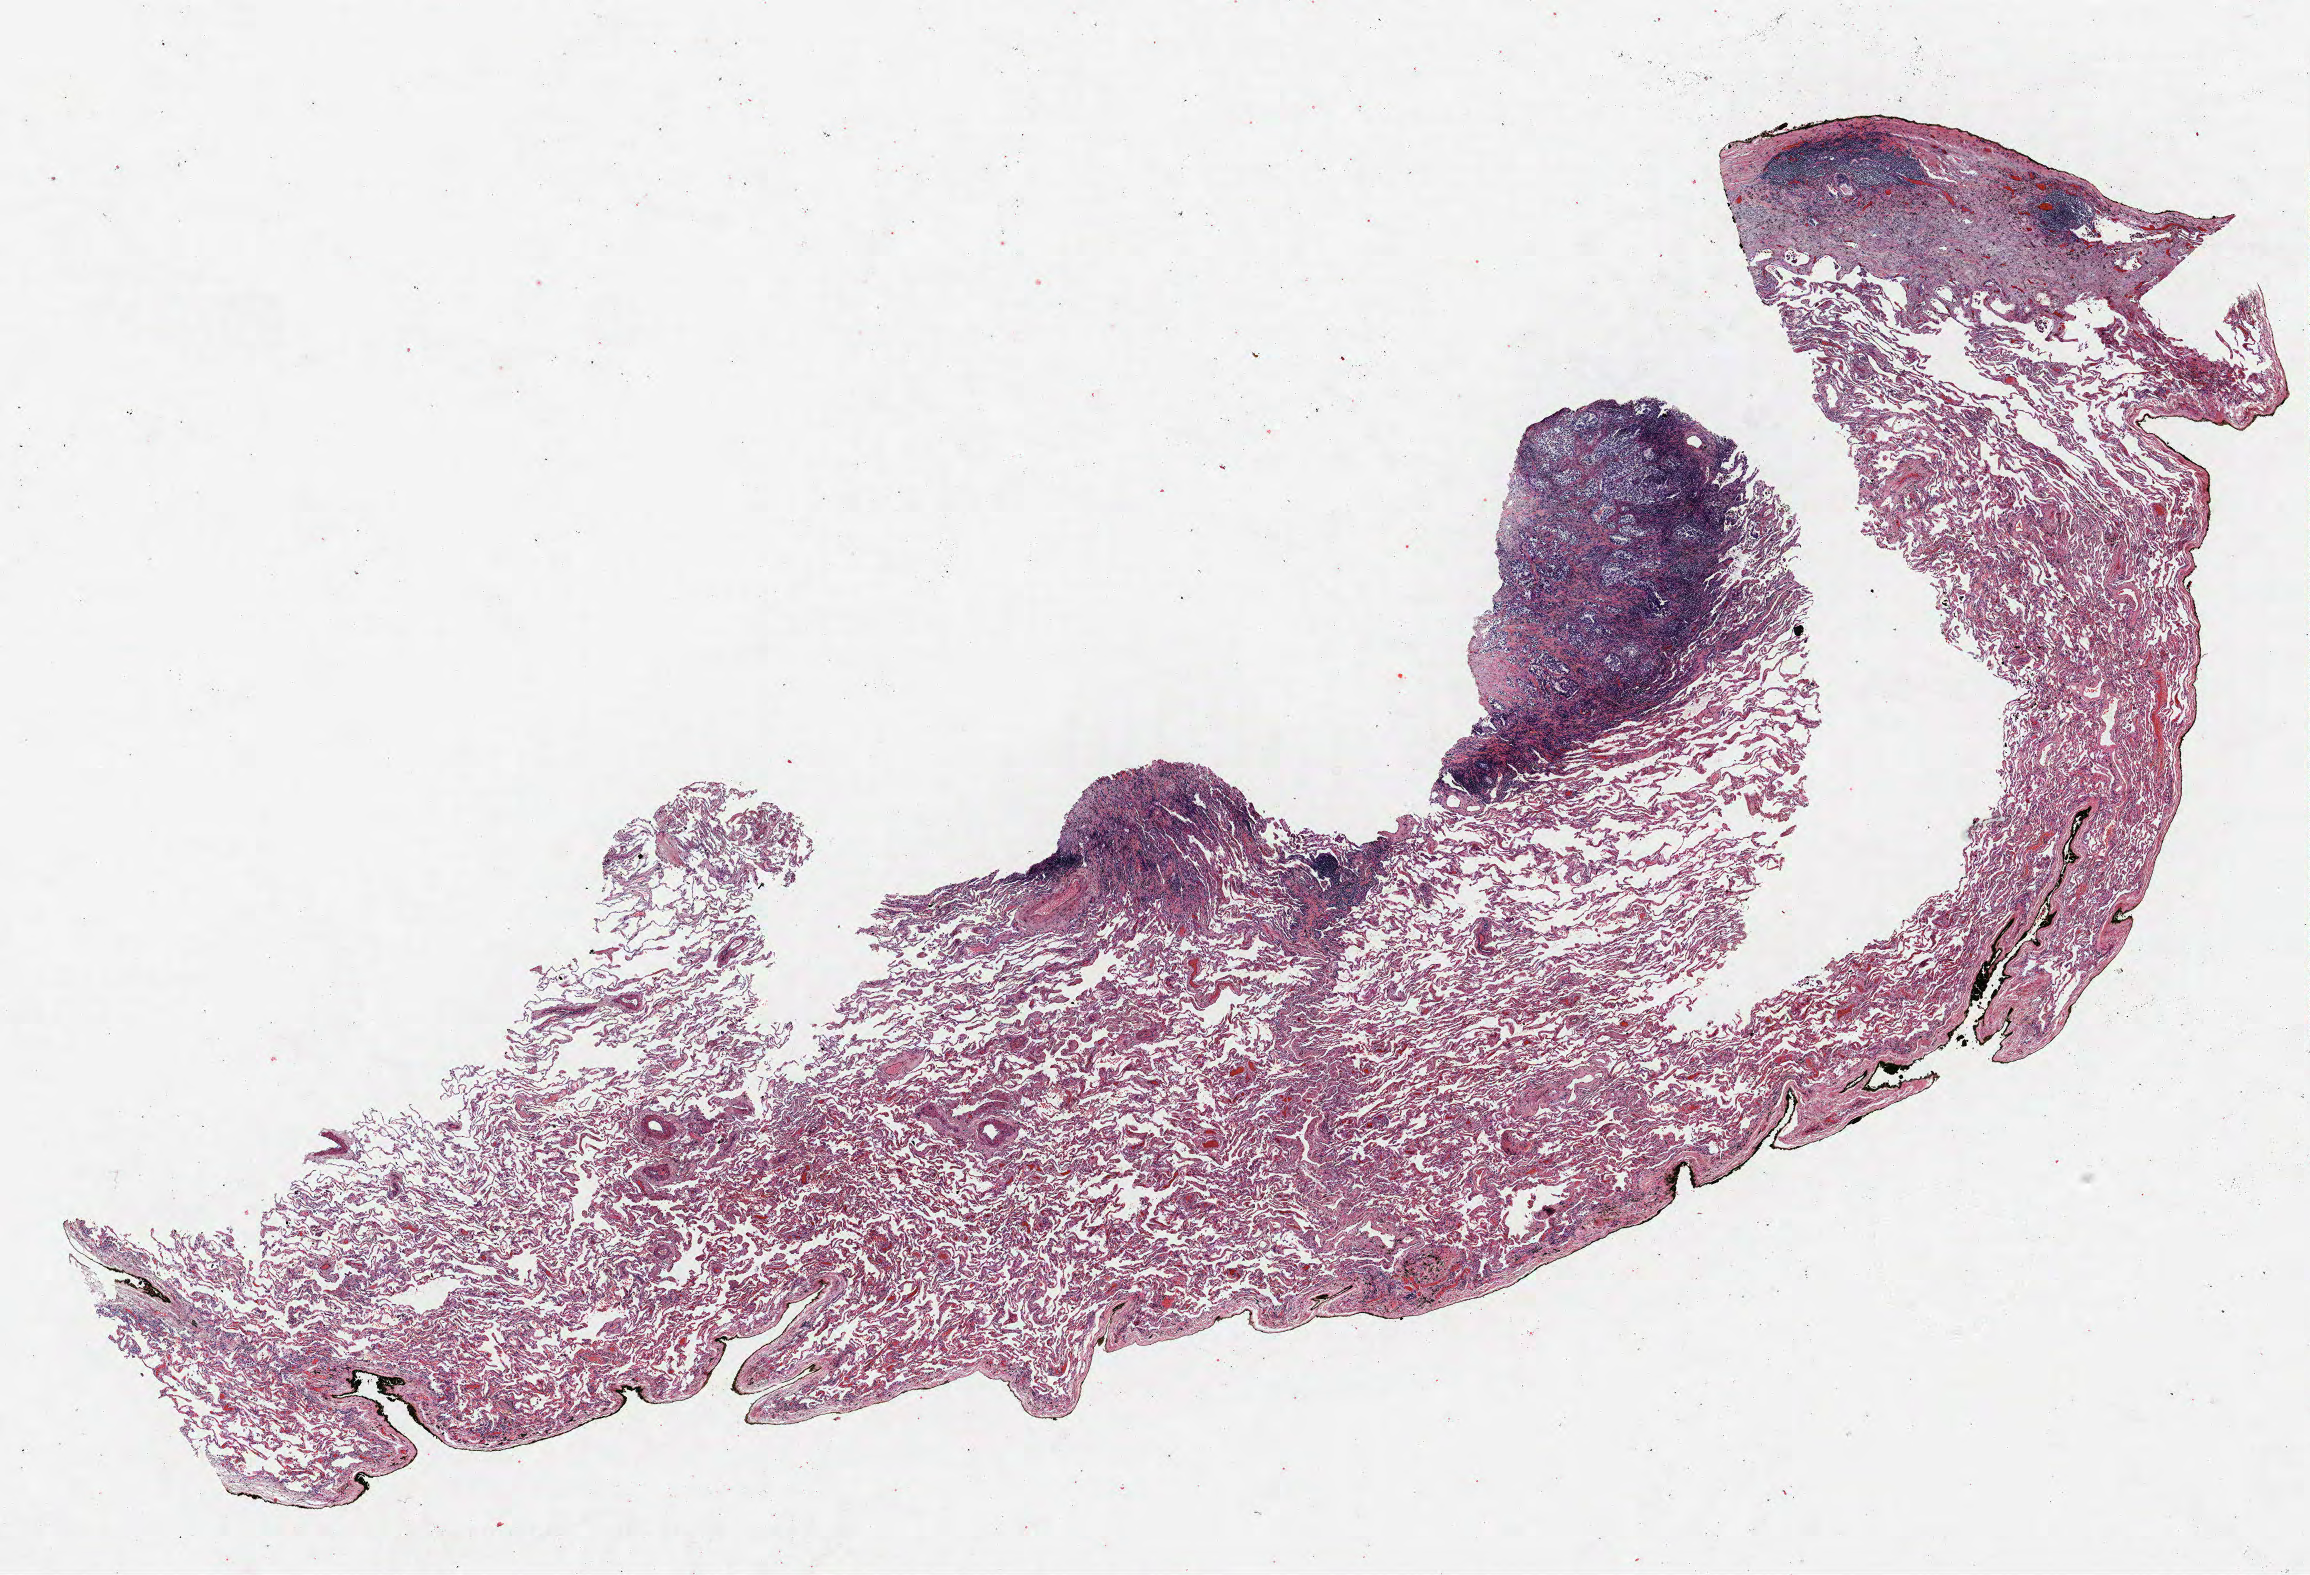
Whole-slide histology image, H&E-stained, shown as a low-resolution overview of the whole scanned area (about 18.5 x 12.6 mm, slide scanned at 40x), FFPE section, lung tissue. Female patient, aged 60 at enrolment.
Participant's lung-cancer diagnosis: Non-small cell carcinoma.